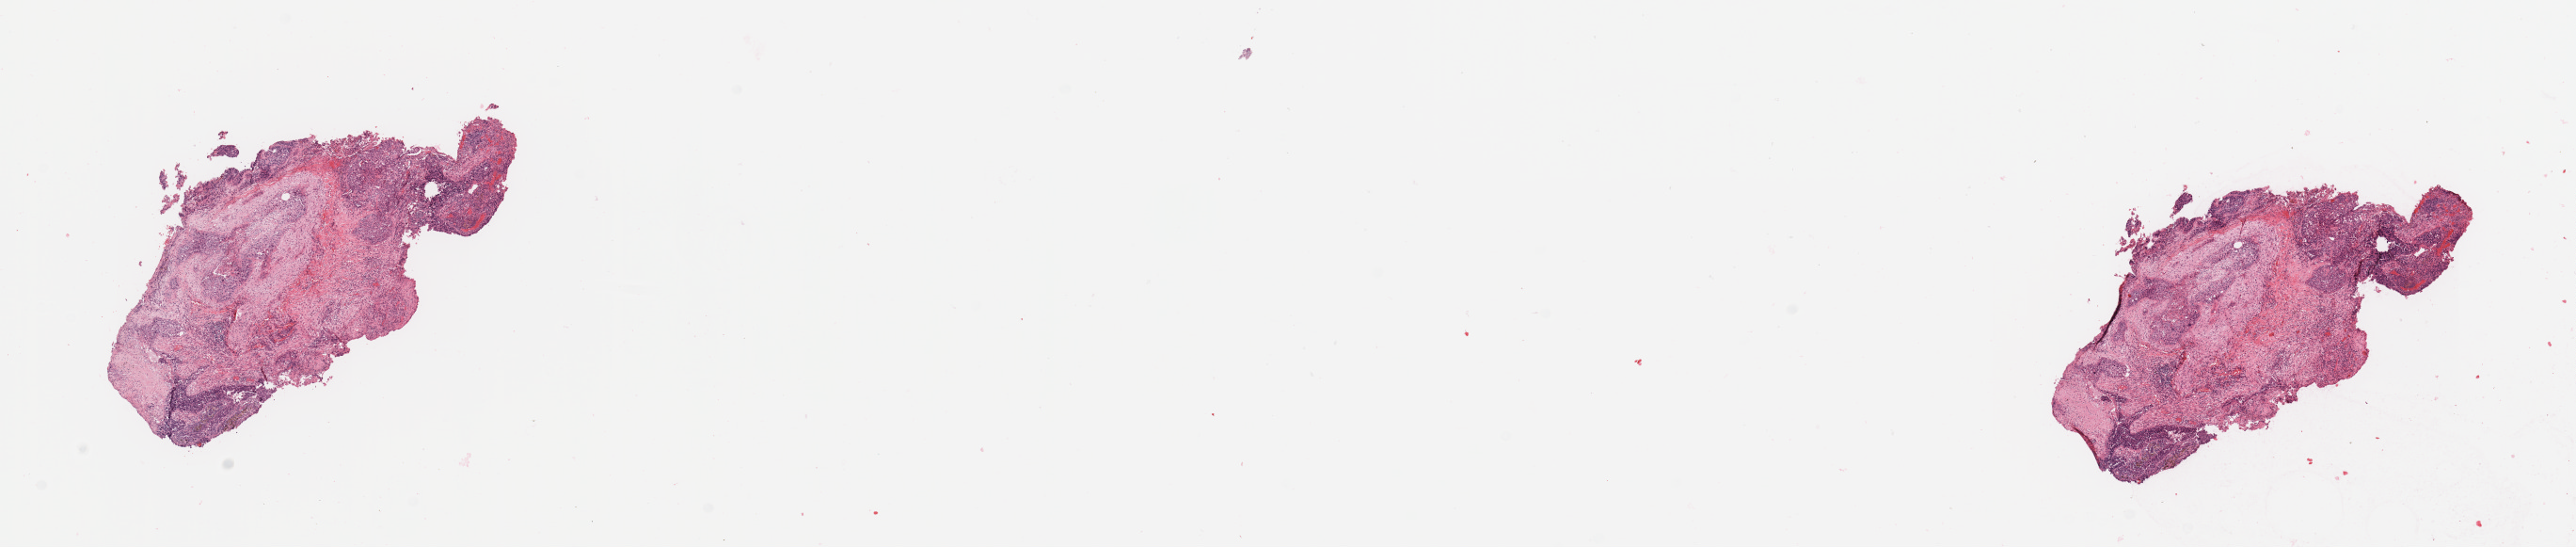
H&E-stained whole-slide image, a low-resolution overview of the entire scanned area, about 21.7 x 4.6 mm. Tumour tissue sample, lung. Patient: female, age 64 years. Histologic grade: G2 (moderately differentiated).
Histologic diagnosis: Squamous cell carcinoma, NOS. Primary tumour site (as recorded): left lower lobe. AJCC pathologic stage: IIB.